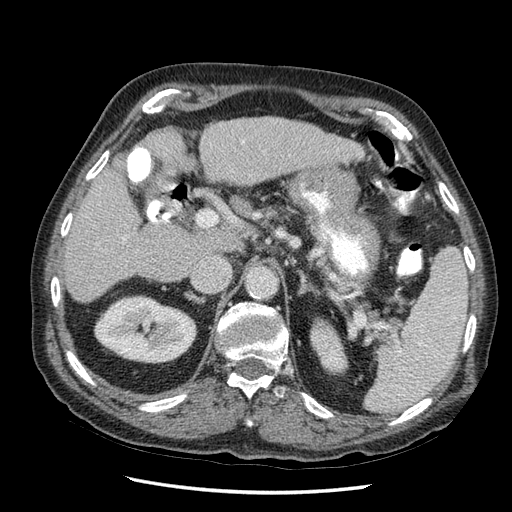
Contrast-enhanced abdominal CT (liver protocol), one axial slice; position 23 of 67 along the scan axis; 120 kVp; soft-tissue window (W 400 / L 40 HU); 512 × 512 image matrix, field of view 360 × 360 mm. From the clinical record (not read from this slice): diagnosis: hepatocellular carcinoma (patient treated with transarterial chemoembolisation; whether this scan precedes or follows treatment is not stated here); TNM stage (as recorded): Stage-I; Child-Pugh class: A; tumour differentiation: moderately differentiated; tumour nodularity: uninodular.
Annotated regions visible in this slice (semi-automatic segmentation, software-assisted and operator-edited):
- liver parenchyma outside the tumour (the mass and vessels are separate outlines, so this box may not span the whole liver): bounding box [x1, y1, x2, y2] px = [64, 118, 360, 300]
- liver vessels: [118, 143, 242, 246]